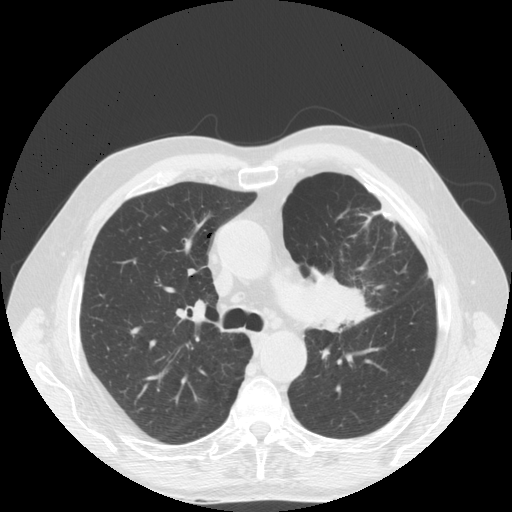
Axial slice from a low-dose chest CT screening exam, baseline screening round, lung window (W 1500 / L -600 HU), slice 55 of 171 in the series. Male participant, aged 70 years at enrolment.
- Lesion marked by an expert reader, bounding box (x1, y1, x2, y2) in pixels: (292, 255, 384, 344).
- Screening reader's record for this exam (one nodule recorded; not confirmed to be the boxed lesion): non-calcified nodule or mass ≥4 mm, left upper lobe, 46 × 31 mm, spiculated (stellate) margins, soft tissue attenuation.
- Later outcome: lung cancer diagnosed 78 days after this screen — squamous cell carcinoma, NOS, left upper lobe, poorly differentiated (G3), stage IIIB (AJCC 6th edition), 46 mm at pathology.